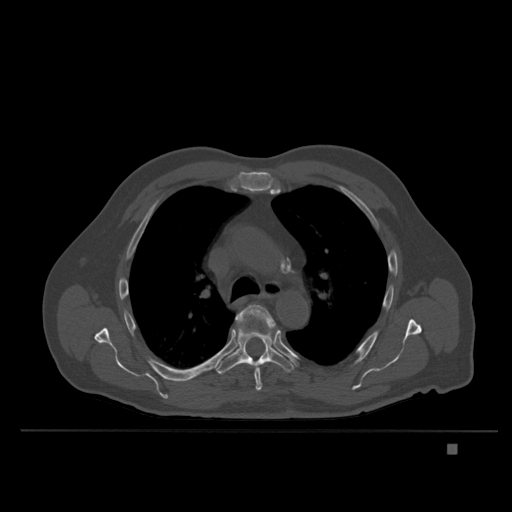
CT including the spine, one axial slice. Slice 265 of 435 in the series (ordered by position). Bone window (W 1800 / L 400 HU). 1.5 mm slice thickness. 512 × 512 image matrix, field of view 434 × 434 mm. Male patient, age 73 years. From the clinical record (not read from this slice): primary cancer: skin.
Annotated regions visible in this slice (semi-automatic segmentation, software-assisted and operator-edited):
- T5 vertebra: box from (x=236, y=304) to (x=274, y=391) px
- T6 vertebra: (x=214, y=326)–(x=294, y=375)
- T7 vertebra: (x=236, y=342)–(x=239, y=347)